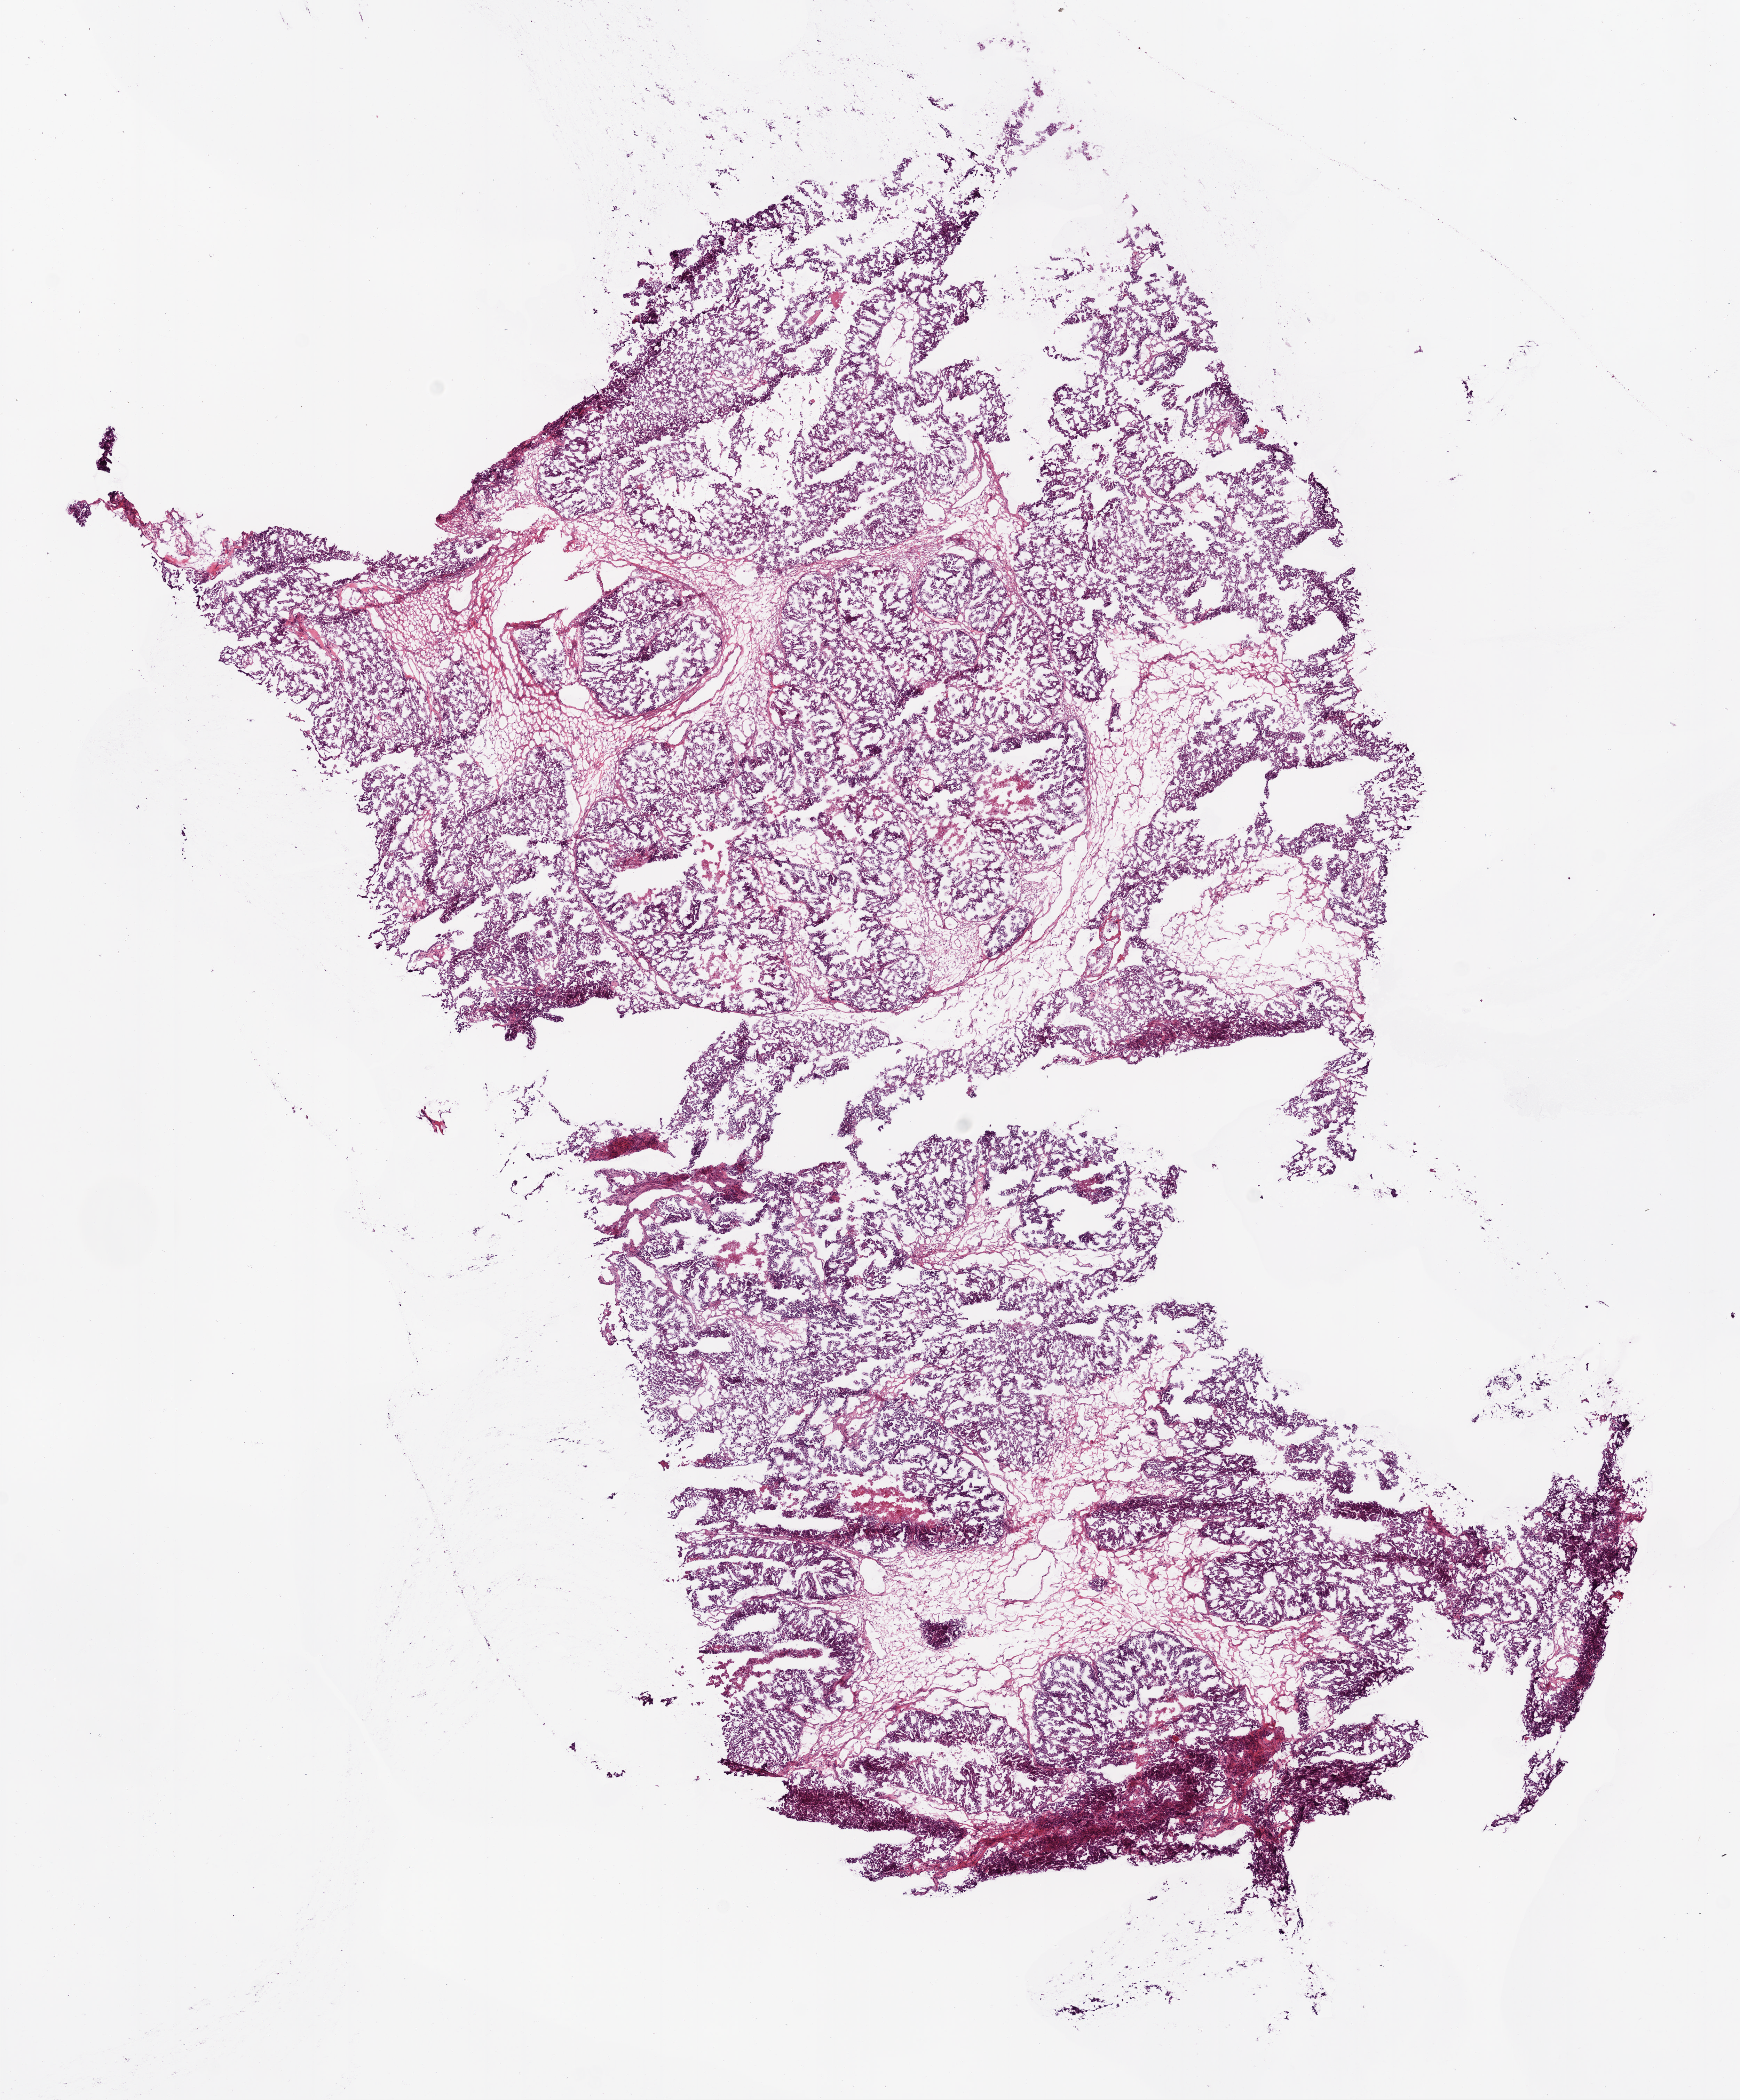
Digitized H&E tissue section (whole slide), whole scanned area (about 10.0 x 12.1 mm, from a 20x scan) shown as a low-resolution overview. Frozen section. Ovary, primary tumour sample. Female patient; age at initial diagnosis 53 years. Histologic grade: G3 (poorly differentiated). Slide review estimates, as recorded: tumour cells 88%, tumour nuclei 85%, normal cells 0%, stromal cells 10%, necrosis 2%.
- FIGO stage: IIIC
- pathologic diagnosis: Serous cystadenocarcinoma, NOS